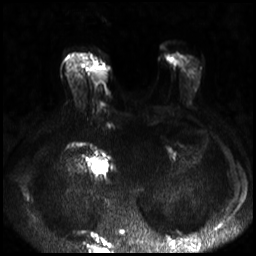
Breast MRI, one axial slice. Slice 8 of 30 in the series (ordered by position). Diffusion-weighted series; image 2 of 4 stored at this slice position (different b-values; order by instance number). 3 T. 4 mm slice thickness. 256 × 256 image matrix, field of view 320 × 320 mm. Female patient.
Structures marked on this image (outlined manually by an expert reader):
- tumour on diffusion-weighted imaging: bounding box <92,66,106,81> (left, top, right, bottom; pixels)